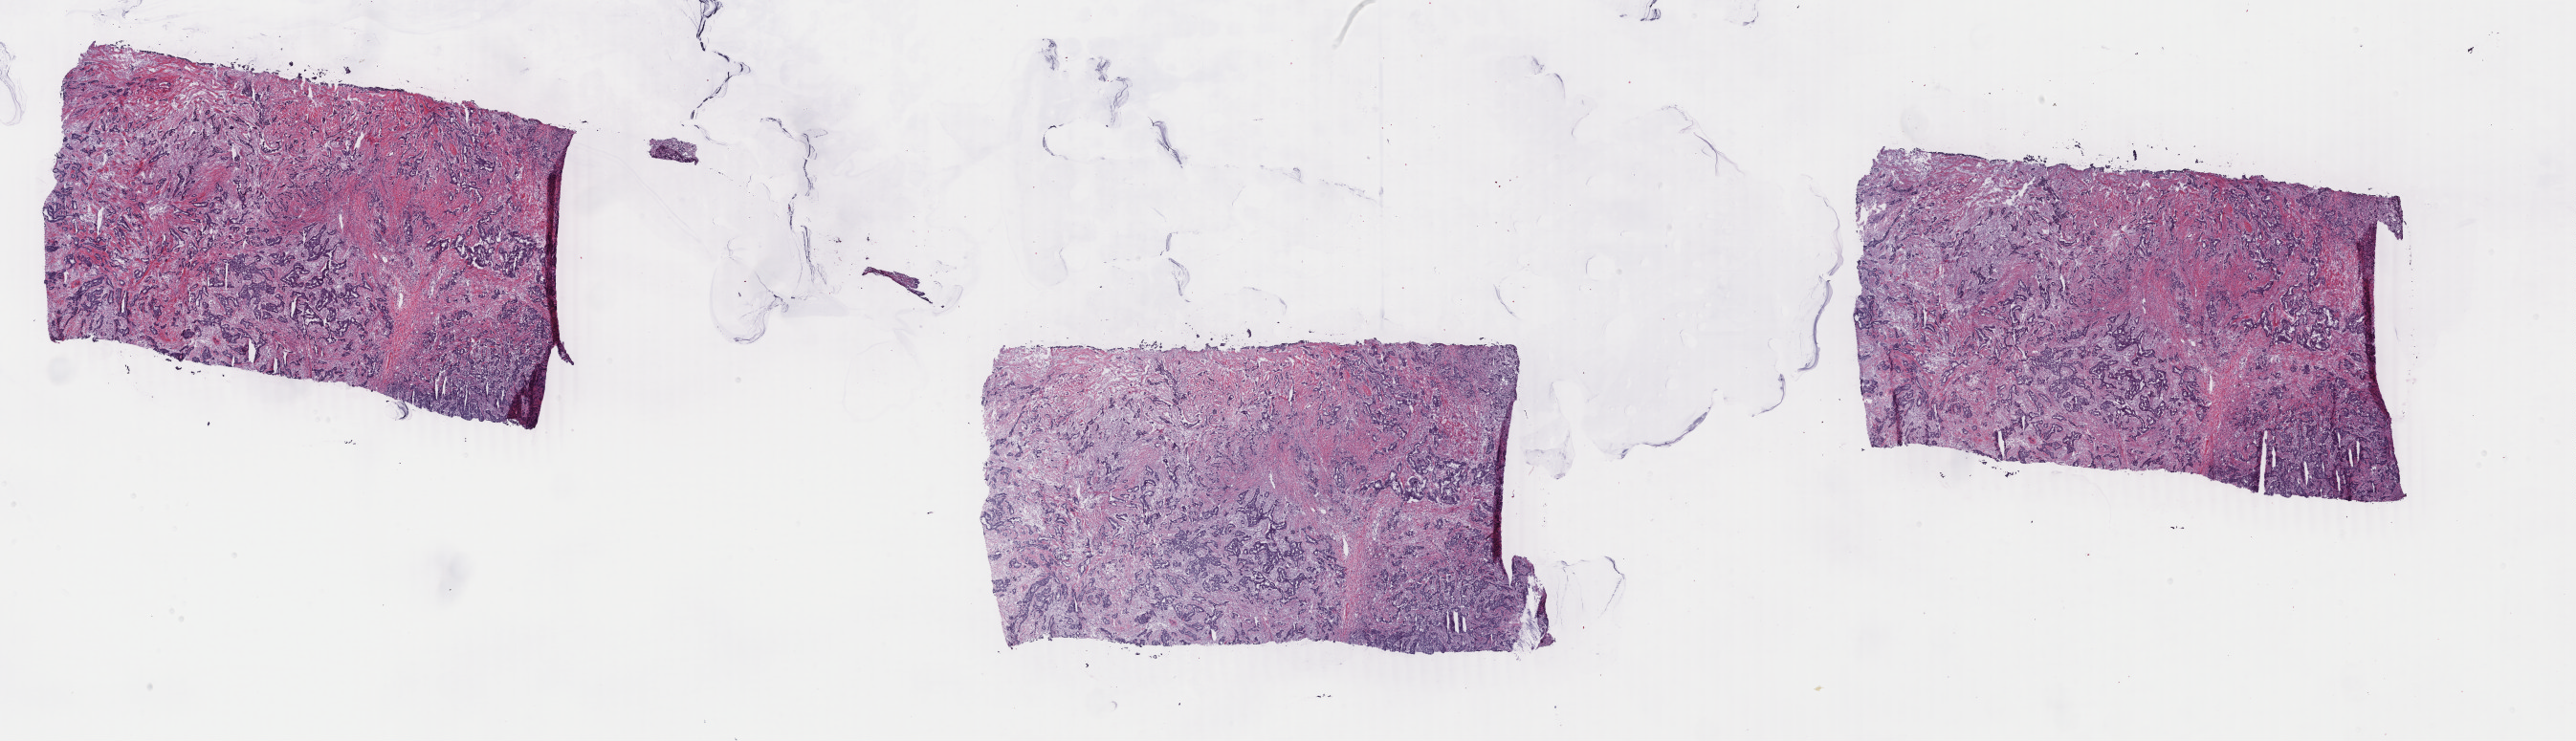
Whole-slide histology image, Hematoxylin and eosin (H&E) stained — whole scanned area (about 42.8 x 12.3 mm, from a 40x scan) shown as a low-resolution overview; frozen section from the top of the tissue portion; primary tumour sample from the breast. Female patient; age at initial diagnosis 71 years. Pathologist review of this section (percent, as recorded): tumour cells 85%, tumour nuclei 85%, normal cells 0%, stromal cells 15%, necrosis 0%. Infiltration values recorded for this section: lymphocyte infiltration 2%, monocyte infiltration 0%, neutrophil infiltration 0%.
Histologic diagnosis: Infiltrating duct carcinoma, NOS. TNM: T2 N0 M0. Lymph nodes positive (case pathology): 0 of 14 examined. Laterality: left. AJCC pathologic stage: IIA.